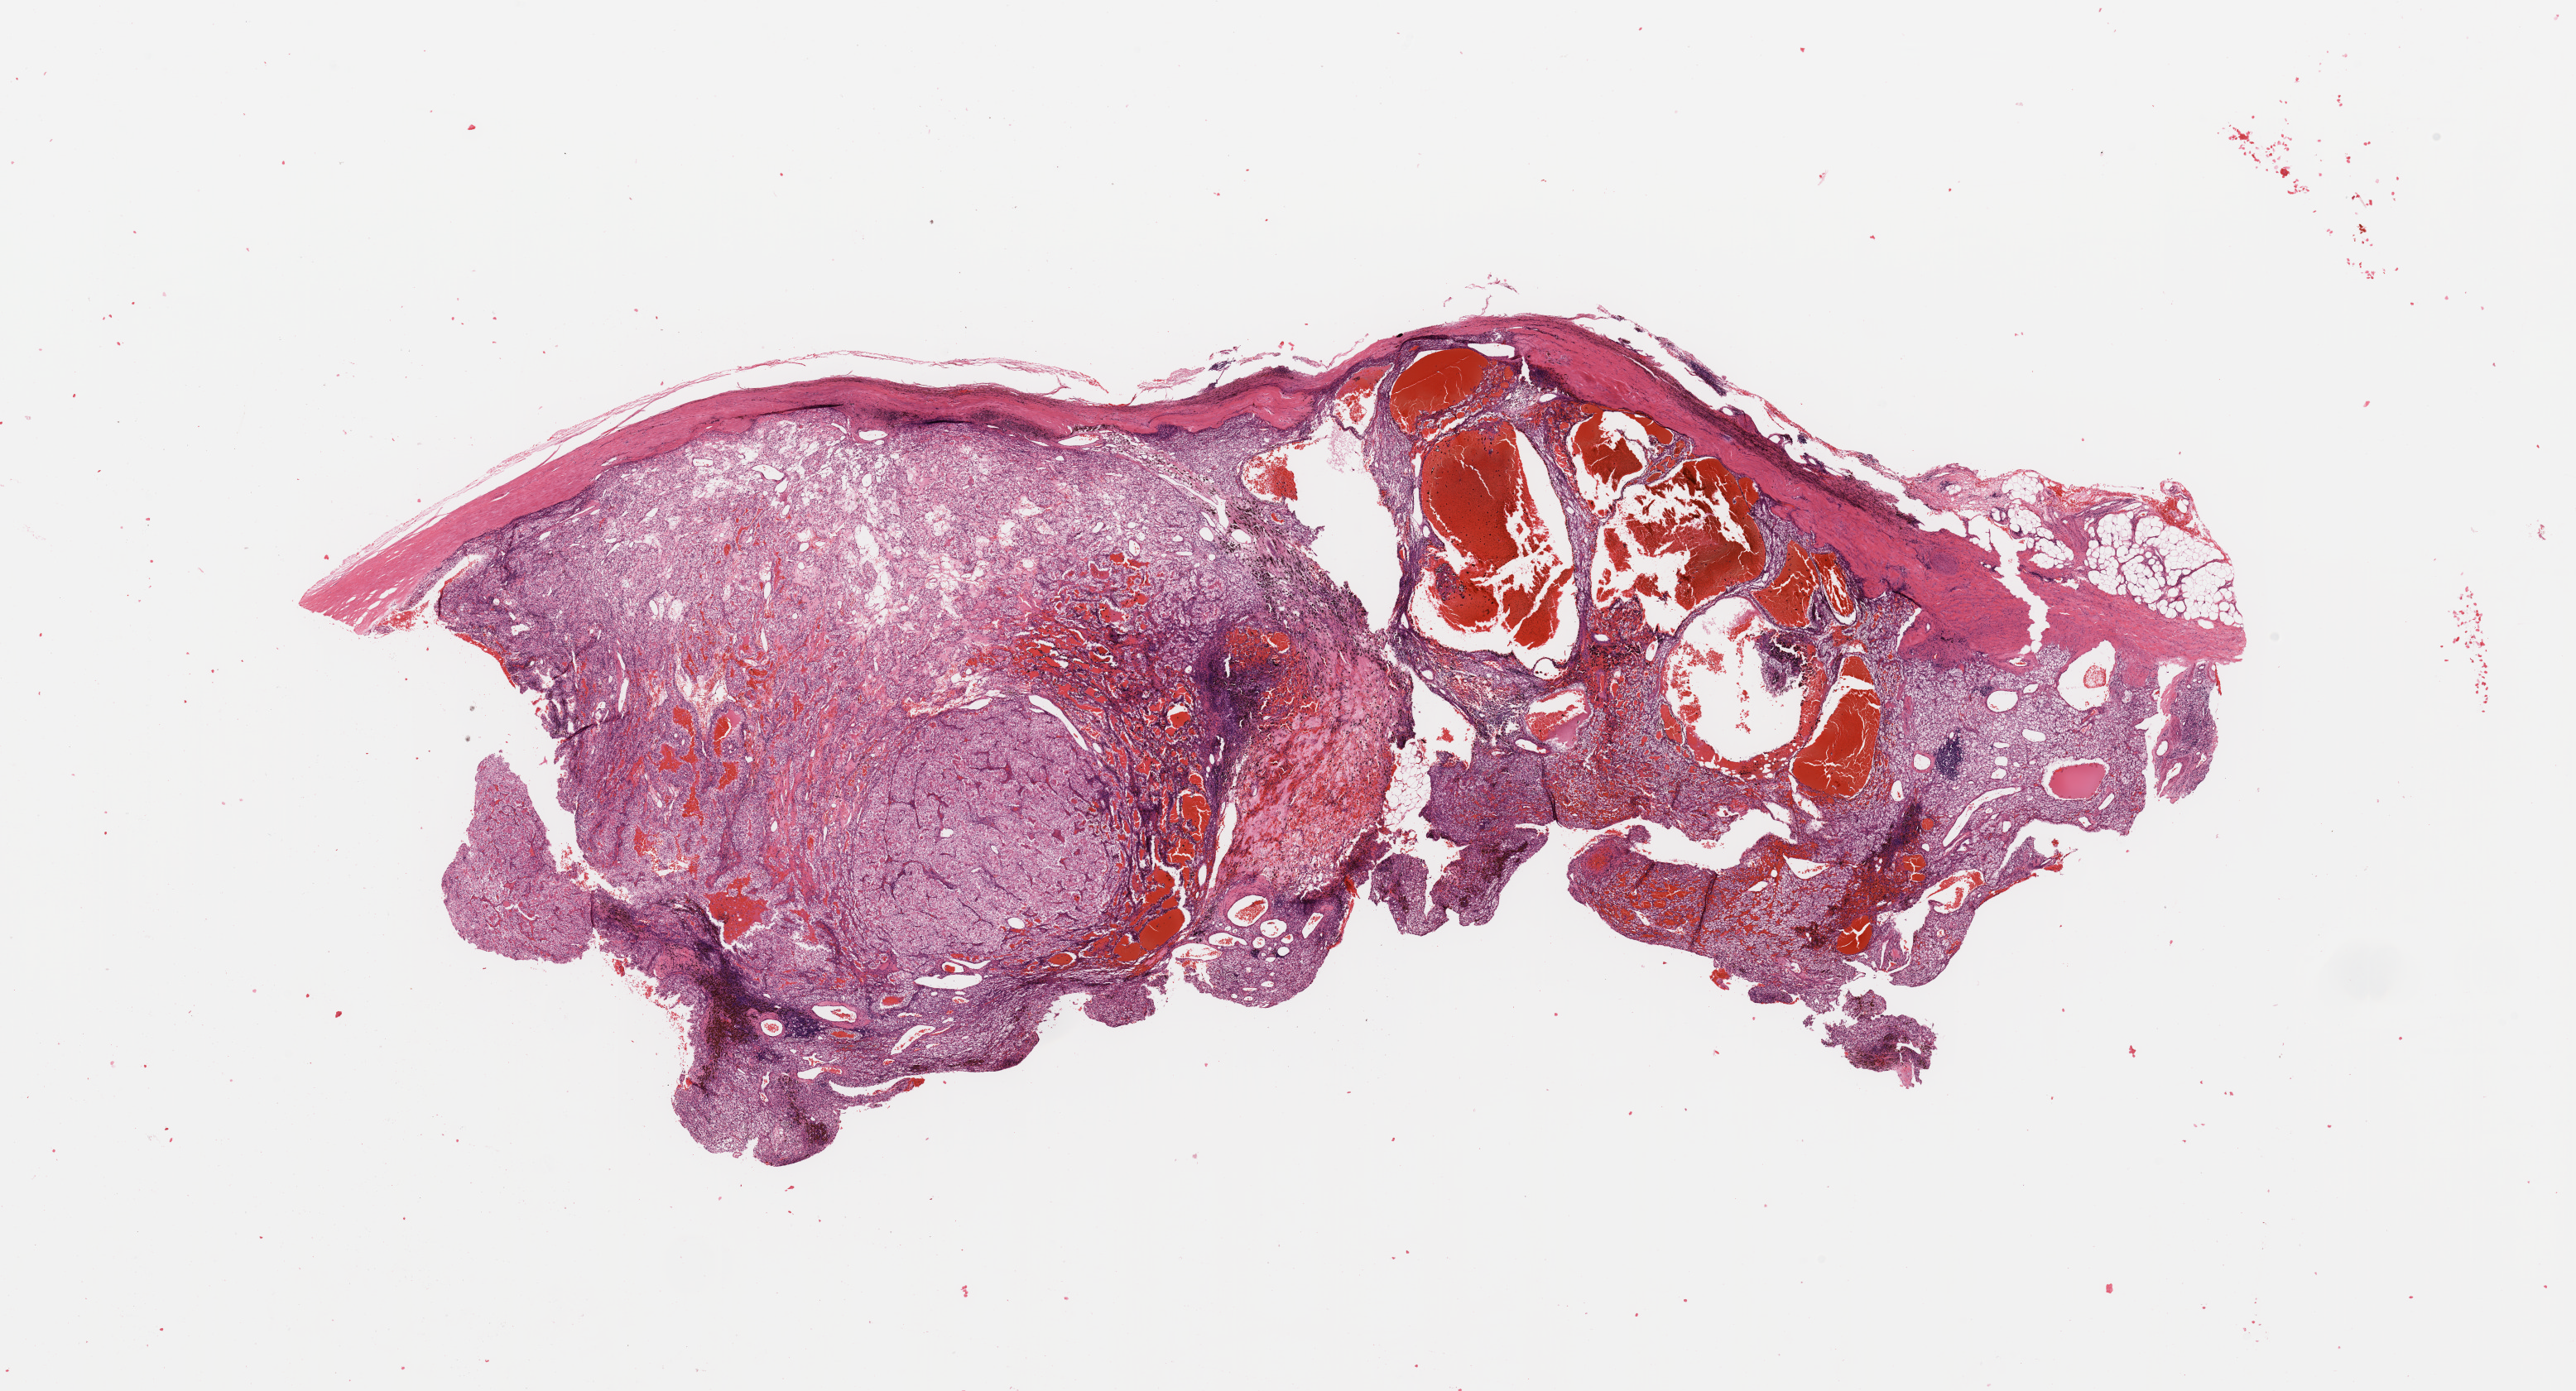
Hematoxylin and eosin (H&E) stained whole-slide image, low-resolution overview of the scanned area, about 24.6 x 13.3 mm; tumour tissue sample, kidney. Patient: male, age 61 years. Histologic grade: G2 (moderately differentiated).
- diagnosis: Renal cell carcinoma, NOS